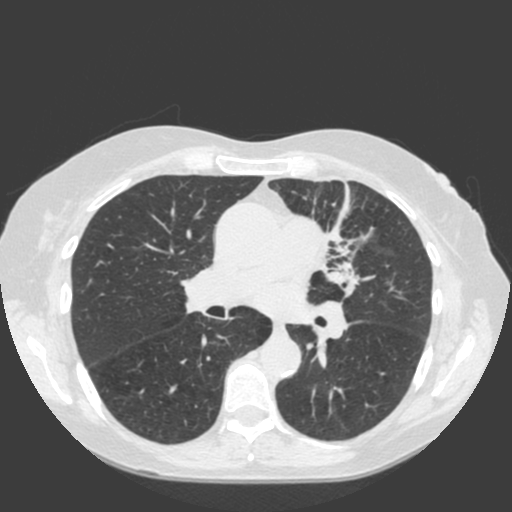
Low-dose screening chest CT, one axial slice; 120 kVp; lung window (W 1500 / L -600 HU); 2 mm slice thickness; 512 × 512 image matrix, field of view 350 × 350 mm.
Structures marked on this image (expert manual segmentation):
- lesion 1 (tumor, hilum of left lung): bounding box <324,227,355,286> (left, top, right, bottom; pixels)